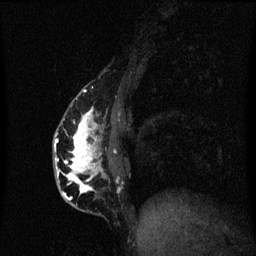
Breast MRI (dynamic contrast-enhanced), one sagittal slice. Dynamic contrast-enhanced series, image 2 of 3 at this slice position (ordered by acquisition). 1.5 T. TE 4.2 ms, TR 8.4 ms. 2 mm slice thickness. 256 × 256 image matrix, field of view 200 × 200 mm. Patient: female, 40 years.
Structures marked on this image (semi-automatically segmented with operator editing):
- analysis volume of interest (the breast-tissue region the enhancement analysis was run in; not a lesion): bounding box (x1, y1, x2, y2) in pixels: (54, 84, 115, 211)
- tumour enhancement mask (voxels above the 70 % enhancement threshold inside the analysis volume of interest): (55, 94, 104, 199)